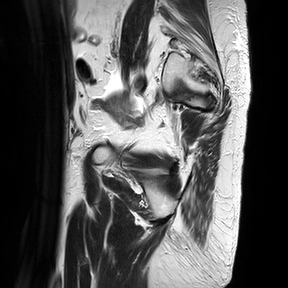
Pelvic MRI for cervical cancer, one sagittal slice. T2-weighted. 1.5 T. TE 100 ms, TR 4816.3 ms. 288 × 288 image matrix, field of view 300 × 300 mm. Patient: female, 74 years.
Outlined on this slice (outlined manually by an expert reader):
- uterus and cervix: bounding box [x1, y1, x2, y2] px = [105, 88, 134, 127]